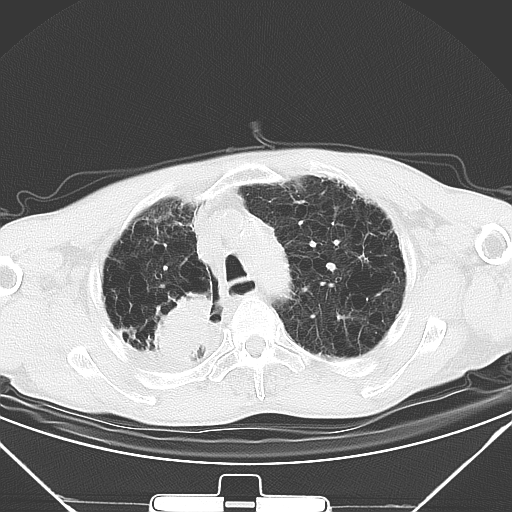
Chest CT, one axial slice; slice 38 of 50 in the series (ordered by position); 120 kVp; lung window (W 1500 / L -600 HU); 5 mm slice thickness; 512 × 512 image matrix. Patient: male, 65 years. Case-level facts recorded for this patient, not image findings: clinical TNM (as recorded): T3 N1 M1a.
Outlined on this slice (rectangle marked by the reading radiologist):
- lung tumour (recorded histology: squamous cell carcinoma): bounding box [x1, y1, x2, y2] px = [147, 292, 210, 368]